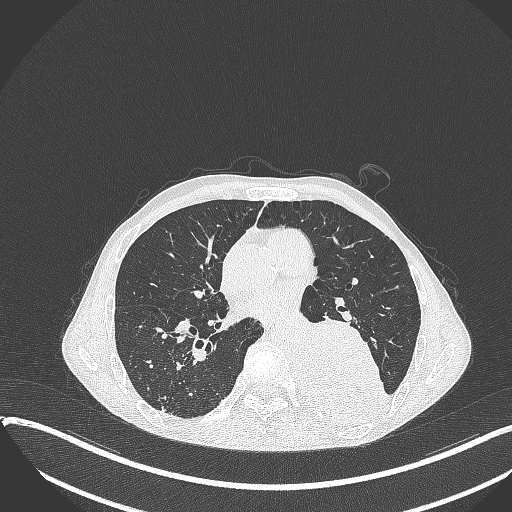
Chest CT, one axial slice; position 178 of 401 along the scan axis; lung window (W 1500 / L -600 HU); 1 mm slice thickness; 512 × 512 image matrix, field of view 400 × 400 mm. Male patient, age 57 years. Case-level facts recorded for this patient, not image findings: clinical TNM (as recorded): T4 N0 M0.
Structures marked on this image (bounding box drawn by a radiologist):
- lung tumour (recorded histology: squamous cell carcinoma): bounding box (x1, y1, x2, y2) in pixels: (294, 318, 390, 426)